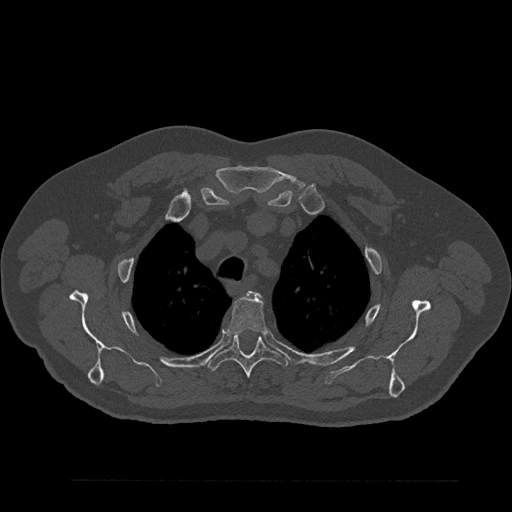
CT including the spine, one axial slice; slice 662 of 797 in the series (ordered by position); reconstruction kernel Br40s/3; bone window (W 1800 / L 400 HU); 0.5 mm slice thickness; 512 × 512 image matrix, field of view 430 × 430 mm. Male patient, age 61 years. From the clinical record (not read from this slice): primary cancer: prostate.
Structures marked on this image (semi-automatic segmentation, software-assisted and operator-edited):
- T2 vertebra: bounding box [x1, y1, x2, y2] px = [255, 293, 259, 296]
- T3 vertebra: [228, 296, 267, 335]
- T4 vertebra: [207, 334, 288, 378]